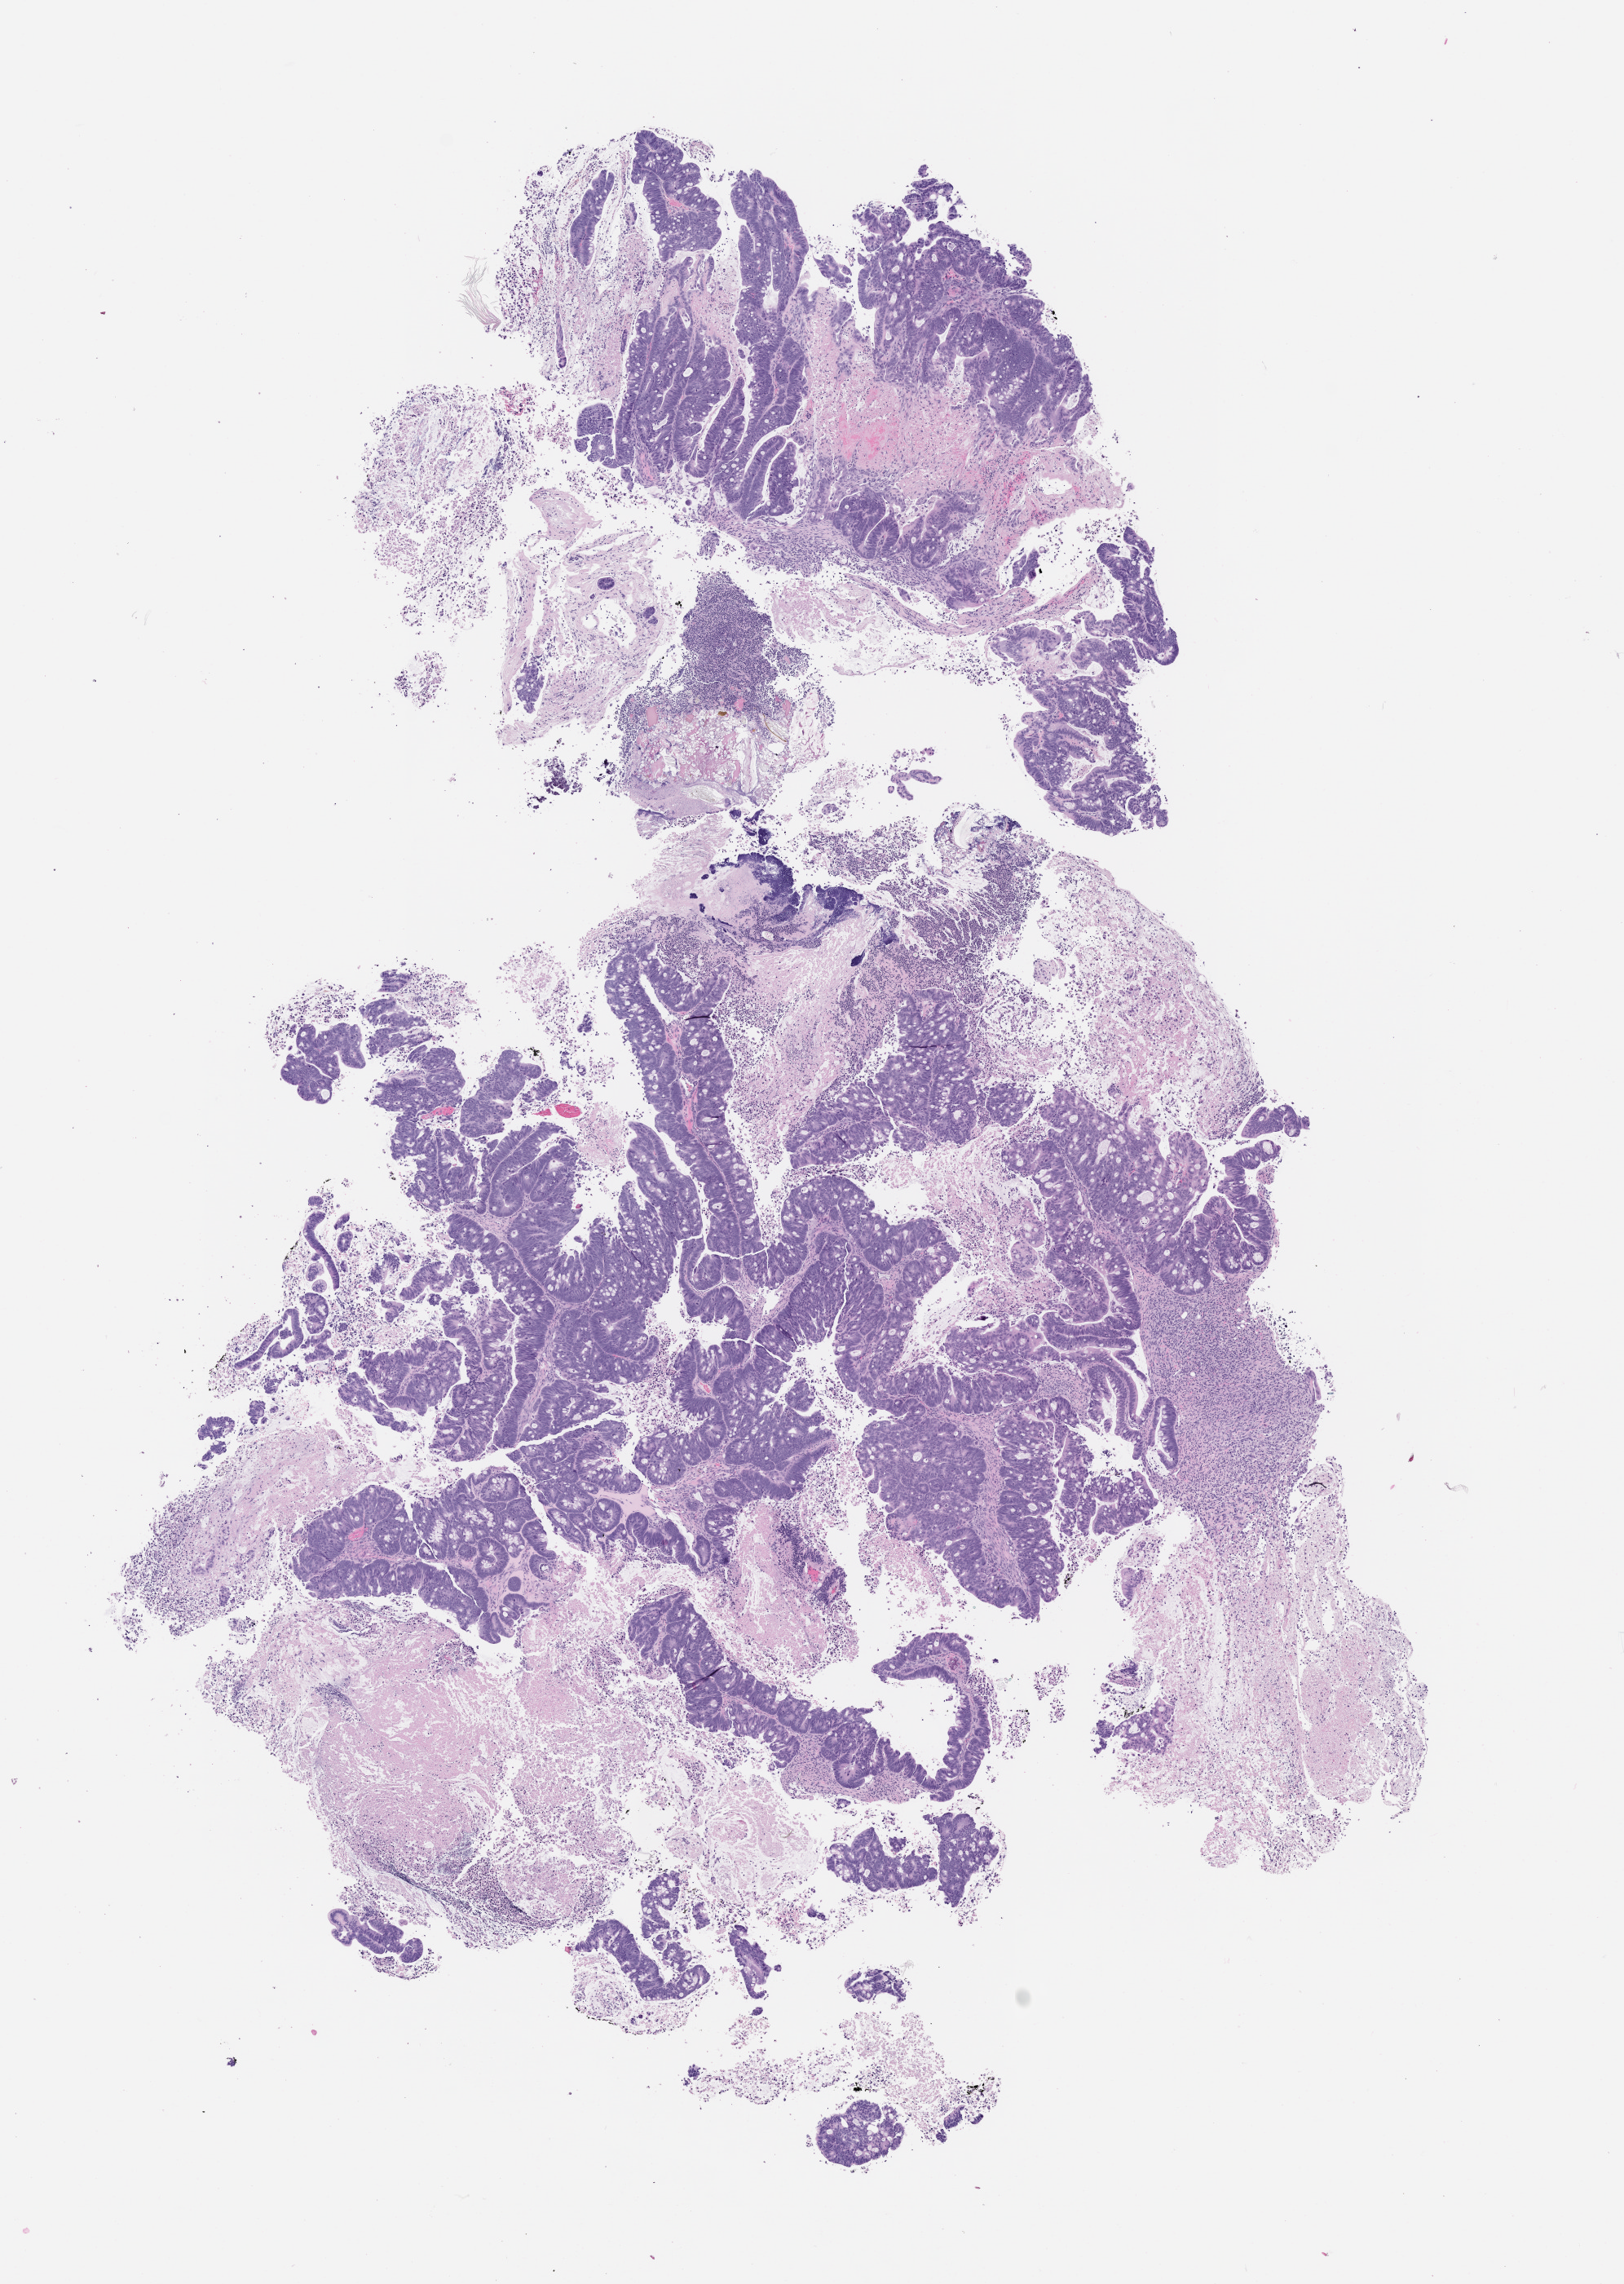
Hematoxylin and eosin (H&E) whole-slide image of a patient-derived xenograft (PDX) tumor grown in a mouse, passage 2, shown as a low-resolution overview of the whole scanned area (about 8.0 x 11.3 mm); formalin-fixed, paraffin-embedded (FFPE) tissue; tumor site category: colon.
Originating patient diagnosis: Colon Adenocarcinoma.